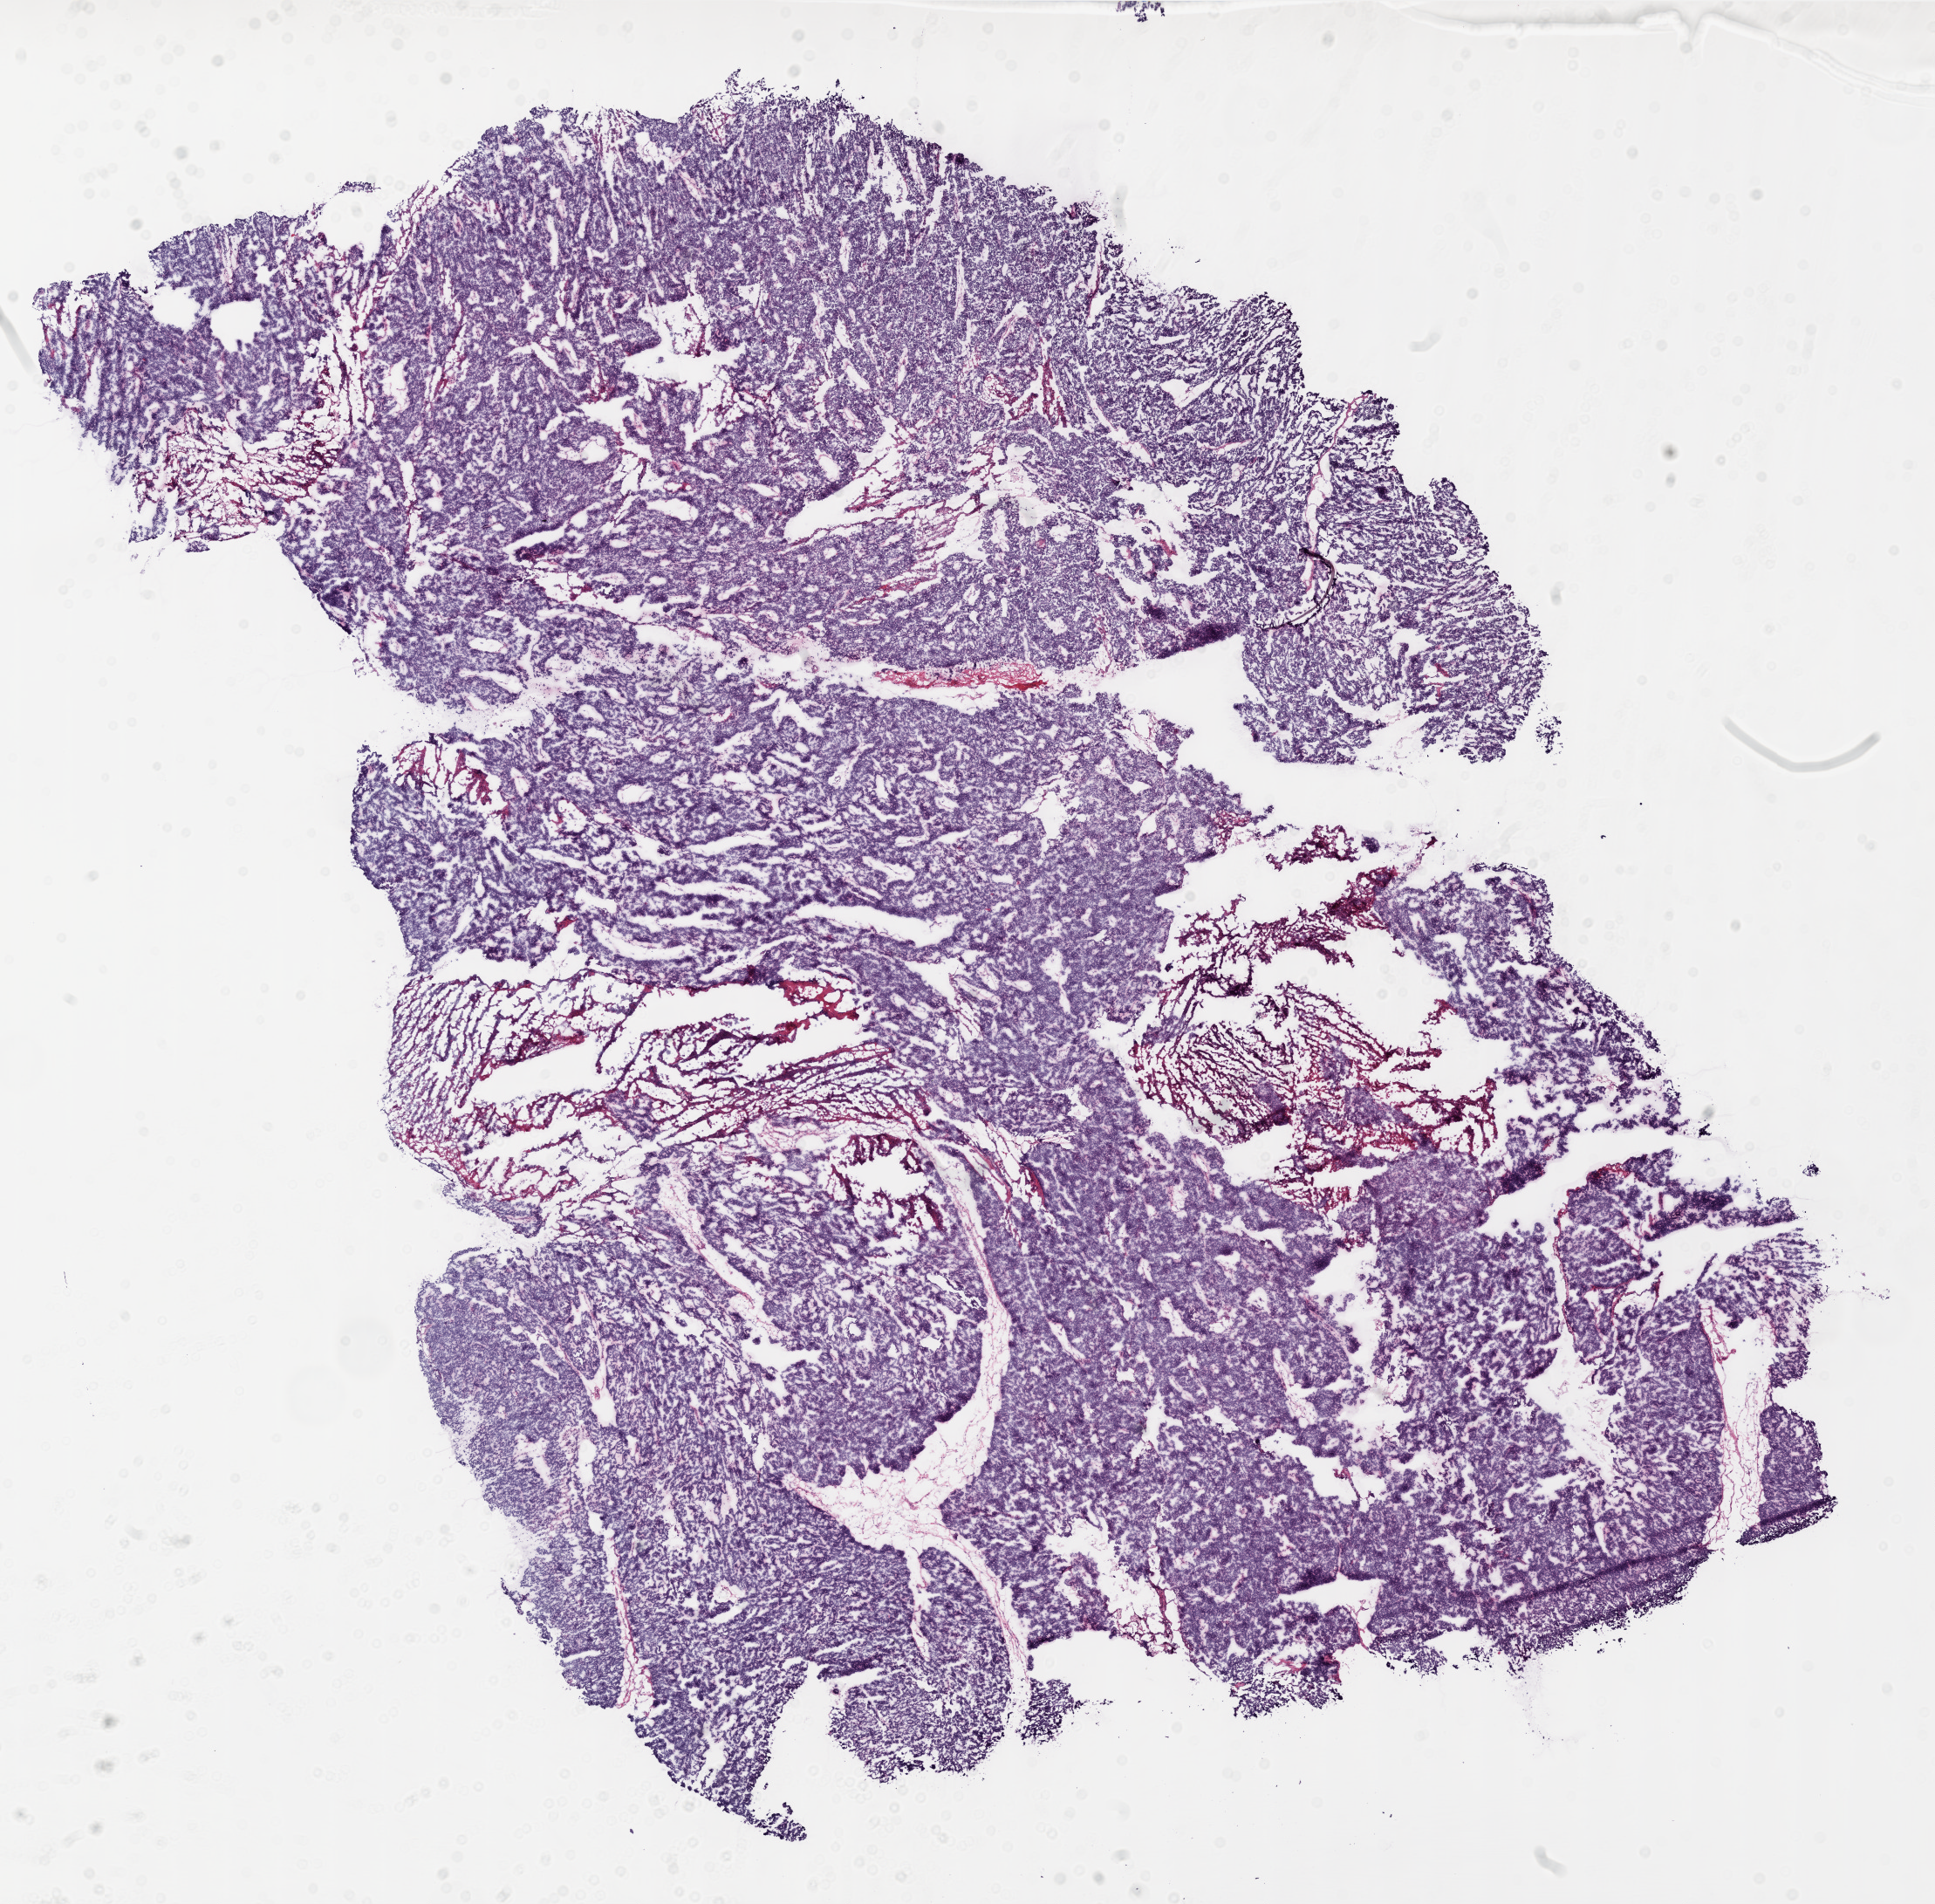
H&E whole-slide image — low-resolution overview of the scanned area, about 17.8 x 17.5 mm. Frozen section. Sample: primary tumour, ovary. Patient: female, age at initial diagnosis 44 years. Histologic grade: G3 (poorly differentiated). Composition of this section per pathologist review: tumour cells 95%, tumour nuclei 98%, normal cells 0%, stromal cells 5%, necrosis 0%.
• diagnosis: Serous cystadenocarcinoma, NOS
• FIGO stage: IIIC